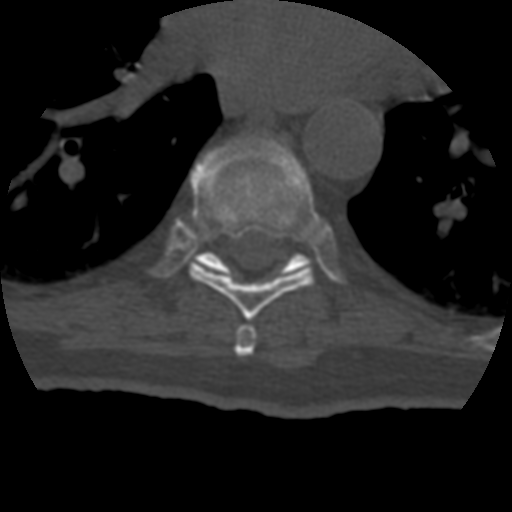
CT including the spine, one axial slice. Position 254 of 399 along the scan axis. 120 kVp. Bone window (W 1800 / L 400 HU). 1.25 mm slice thickness. 512 × 512 image matrix, field of view 160 × 160 mm. Patient age 69 years. Case-level facts recorded for this patient, not image findings: primary cancer: prostate.
Outlined on this slice (semi-automatically segmented with operator editing):
- T7 vertebra: bounding box <235,324,256,356> (left, top, right, bottom; pixels)
- T8 vertebra: <189,141,319,321>
- T9 vertebra: <199,251,308,270>